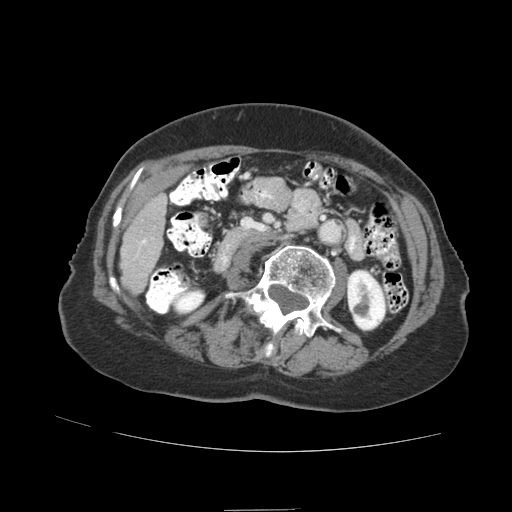
Contrast-enhanced abdominal CT (liver protocol), one axial slice. Position 19 of 89 along the scan axis. Soft-tissue window (W 400 / L 40 HU). 2.5 mm slice thickness. 512 × 512 image matrix, field of view 360 × 360 mm. Case-level facts recorded for this patient, not image findings: diagnosis: hepatocellular carcinoma (patient treated with transarterial chemoembolisation; whether this scan precedes or follows treatment is not stated here); TNM stage (as recorded): Stage-II; Child-Pugh class: A; tumour nodularity: multinodular; tumour size: 4 cm.
Outlined on this slice (semi-automatic segmentation, software-assisted and operator-edited):
- liver parenchyma outside the tumour (the mass and vessels are separate outlines, so this box may not span the whole liver): bounding box [x1, y1, x2, y2] px = [120, 192, 166, 294]
- liver vessels: [141, 239, 146, 244]